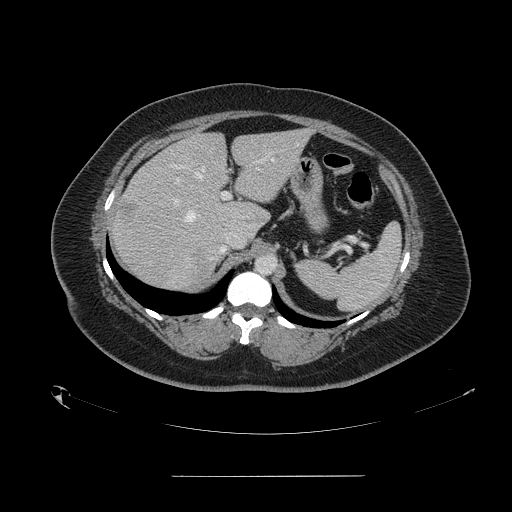
Contrast-enhanced abdominal CT, one axial slice; slice 104 of 164 in the series (ordered by position); intravenous contrast given; soft-tissue window (W 400 / L 40 HU); 2.5 mm slice thickness; 512 × 512 image matrix, field of view 495 × 495 mm. Female patient, age 52 years. From the clinical record (not read from this slice): diagnosis: colorectal cancer liver metastases, imaged before liver resection; multiple liver metastases: yes; largest metastasis: 3.5 cm; chemotherapy before resection: no.
Annotated regions visible in this slice (manually delineated by an expert):
- hepatic veins: bounding box <184,144,298,222> (left, top, right, bottom; pixels)
- liver: <112,130,309,290>
- planned liver remnant (the part of the liver to remain after resection): <174,130,309,229>
- portal vein (with intrahepatic branches): <172,160,262,206>
- liver metastasis: <193,257,210,277>
- liver metastasis: <251,212,262,223>
- liver metastasis: <118,202,135,221>